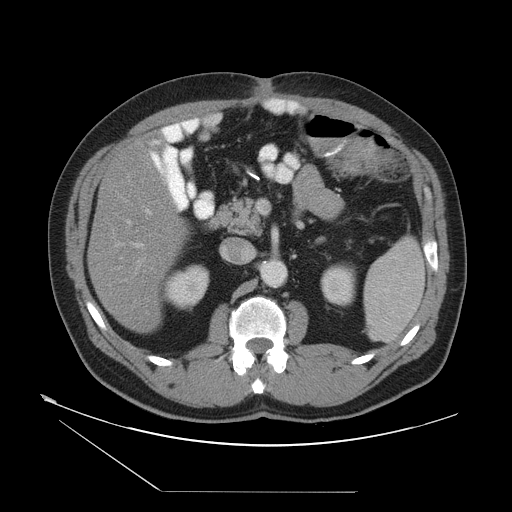
Contrast-enhanced abdominal CT, one axial slice; slice 22 of 55 in the series (ordered by position); reconstruction kernel STANDARD; 120 kVp; intravenous contrast given; soft-tissue window (W 400 / L 40 HU); 5 mm slice thickness; 512 × 512 image matrix, field of view 454 × 454 mm. Male patient, age 59 years. From the clinical record (not read from this slice): diagnosis: colorectal cancer liver metastases, imaged before liver resection; multiple liver metastases: yes; largest metastasis: 0.3 cm.
Structures marked on this image (expert manual segmentation):
- hepatic veins: box from (x=112, y=143) to (x=155, y=301) px
- liver: (x=90, y=143)–(x=184, y=331)
- planned liver remnant (the part of the liver to remain after resection): (x=89, y=143)–(x=185, y=331)
- portal vein (with intrahepatic branches): (x=114, y=210)–(x=151, y=248)